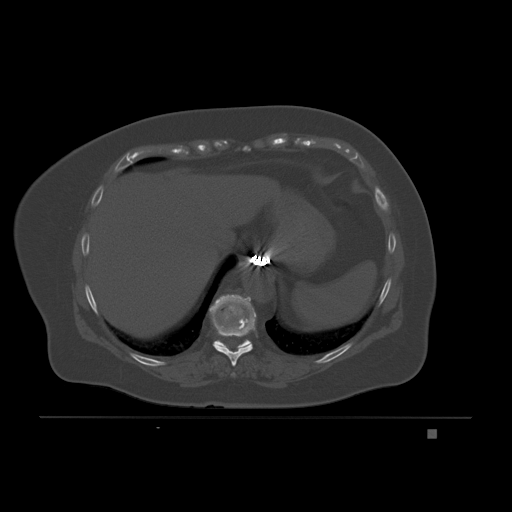
CT including the spine, one axial slice. Position 106 of 221 along the scan axis. Bone window (W 1800 / L 400 HU). 3 mm slice thickness. 512 × 512 image matrix. Female patient, age 63 years. Case-level facts recorded for this patient, not image findings: primary cancer: breast.
Annotated regions visible in this slice (semi-automatic segmentation, software-assisted and operator-edited):
- T10 vertebra: bounding box <209,294,255,350> (left, top, right, bottom; pixels)
- T8 vertebra: <231,373,235,376>
- T9 vertebra: <213,313,255,367>